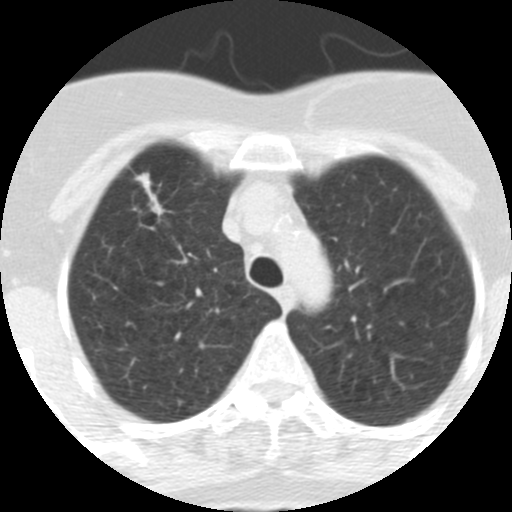
Low-dose screening chest CT, one axial slice; slice 248 of 313 in the series (ordered by position); reconstruction kernel STANDARD; 120 kVp; lung window (W 1500 / L -600 HU); 2.5 mm slice thickness; 512 × 512 image matrix.
Outlined on this slice (expert manual segmentation):
- lesion 1 (tumor, upper lobe of right lung): bounding box [x1, y1, x2, y2] px = [135, 173, 165, 216]